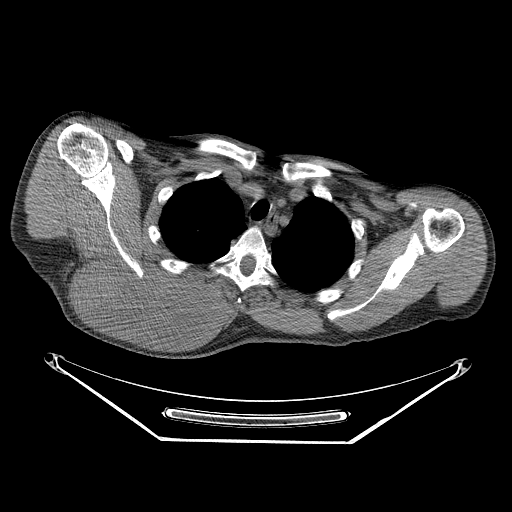
CT of an extremity soft-tissue mass (from a PET/CT study), one axial slice. Position 196 of 267 along the scan axis. Soft-tissue window (W 400 / L 40 HU). 3.75 mm slice thickness. 512 × 512 image matrix. Male patient. From the clinical record (not read from this slice): histological type: pleiomorphic spindle cell undifferentiated; grade: high; site of the primary tumour: right parascapusular.
Structures marked on this image (expert contour drawn on MRI and transferred to this co-registered scan by the dataset authors):
- gross tumour volume including surrounding oedema: box from (x=77, y=258) to (x=234, y=337) px
- gross tumour volume (mass): (x=77, y=258)–(x=218, y=334)